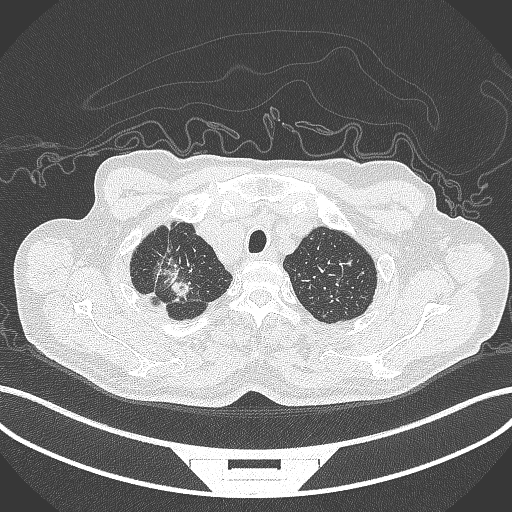
Chest CT, one axial slice; reconstruction kernel B70f; 120 kVp; lung window (W 1500 / L -600 HU); 512 × 512 image matrix. Male patient, age 69 years. From the clinical record (not read from this slice): clinical TNM (as recorded): T1c N1 M1.
Annotated regions visible in this slice (bounding box drawn by a radiologist):
- lung tumour (recorded histology: adenocarcinoma): bounding box (x1, y1, x2, y2) in pixels: (148, 253, 198, 306)